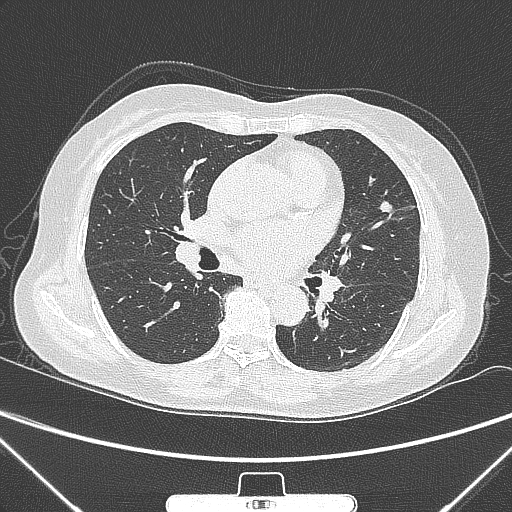
Chest CT, one axial slice; slice 146 of 300 in the series (ordered by position); 120 kVp; lung window (W 1500 / L -600 HU); 1 mm slice thickness; 512 × 512 image matrix, field of view 350 × 350 mm. Female patient, age 70 years. Case-level facts recorded for this patient, not image findings: clinical TNM (as recorded): T1b N0 M0; histopathological grade: G2.
Annotated regions visible in this slice (bounding box drawn by a radiologist):
- lung tumour (recorded histology: adenocarcinoma): bounding box (x1, y1, x2, y2) in pixels: (372, 193, 398, 222)